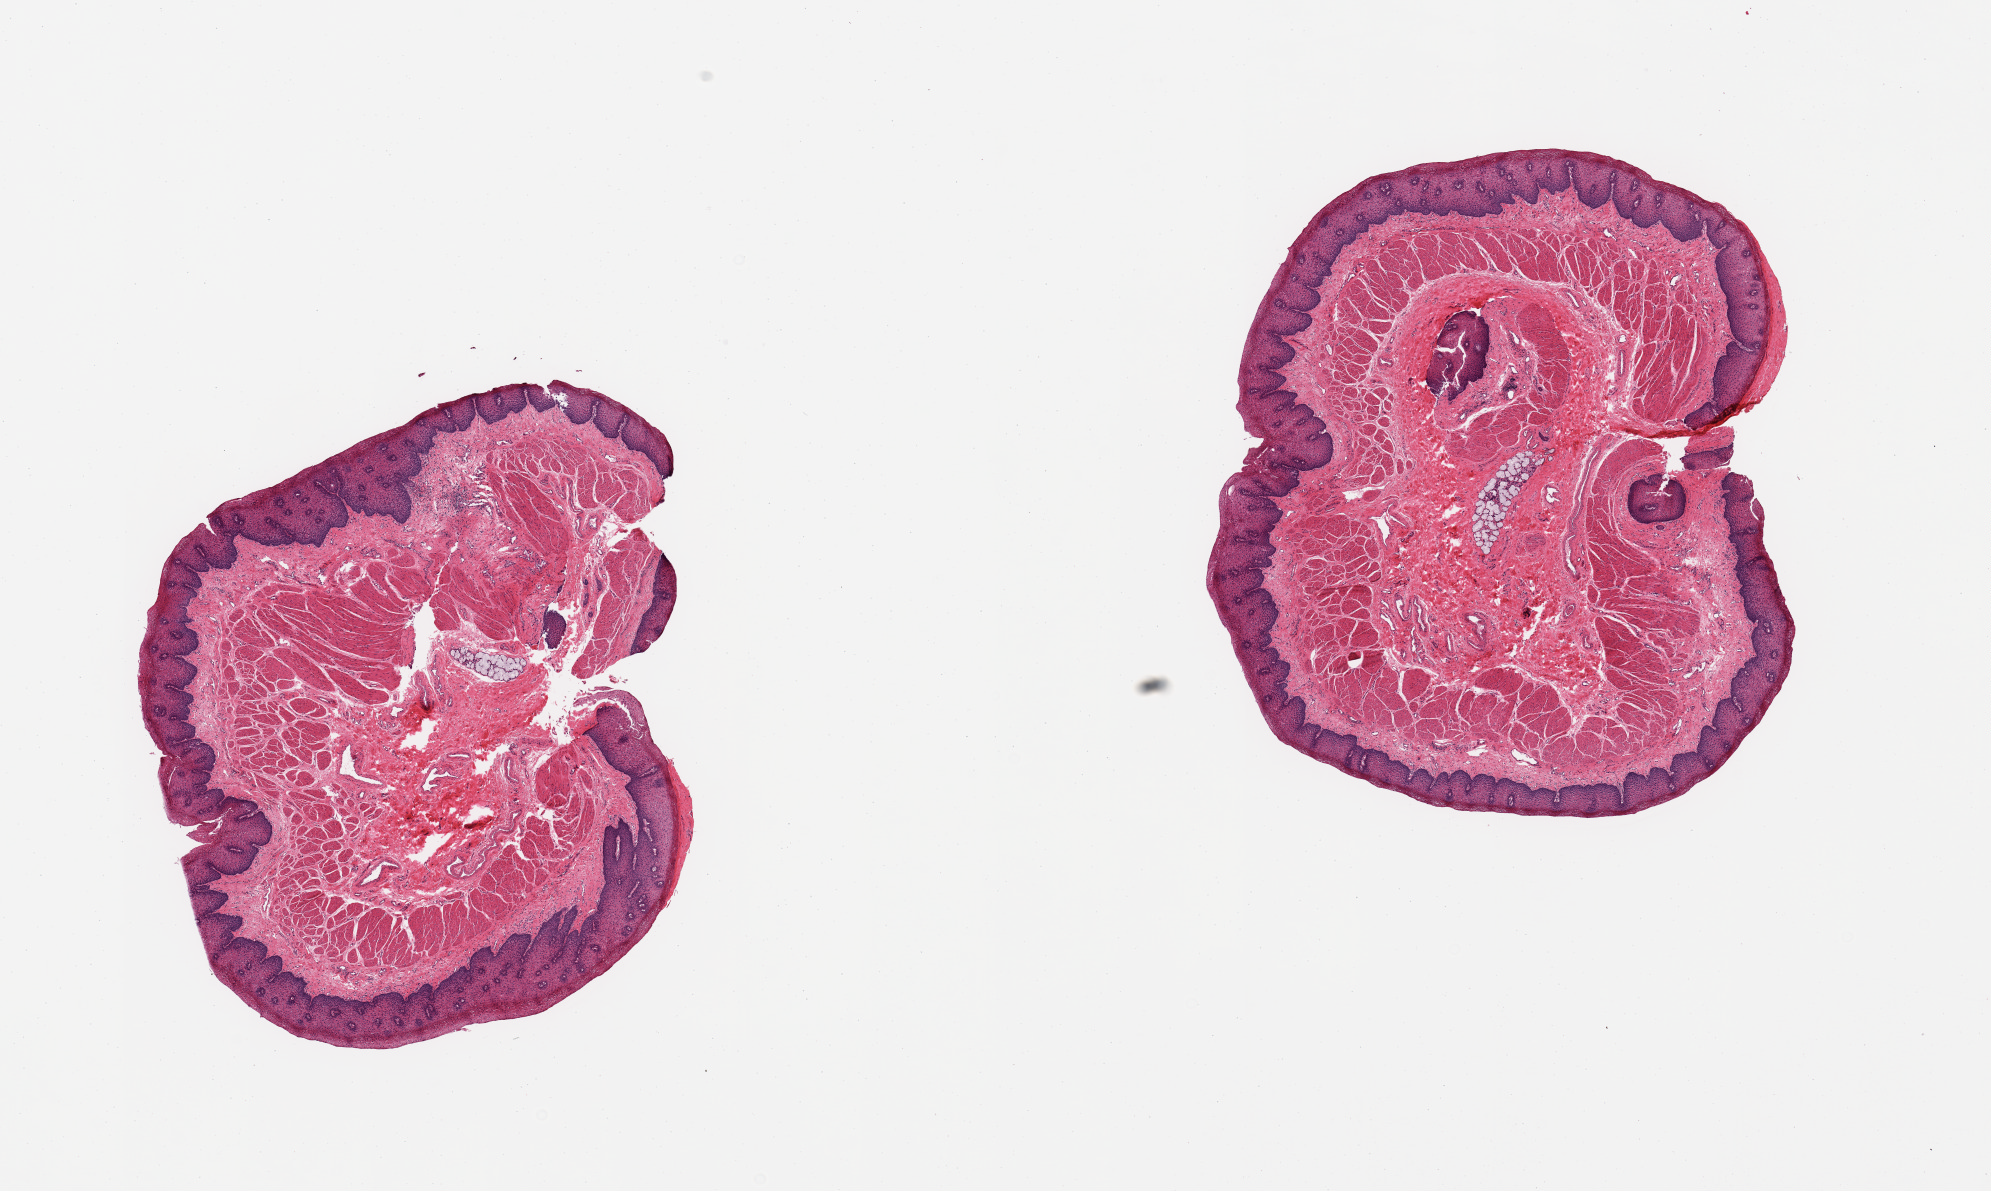
Haematoxylin and eosin whole-slide image — low-resolution overview of the scanned area, about 15.8 x 9.4 mm (acquisition: 20x scan), PAXgene-fixed paraffin-embedded (PFPE) section, section of esophageal mucous membrane (target tissue), tissue donor sample. Donor: male.
* reviewer comment on this tissue sample: 2 pieces, squamous mucosa up to ~0.3mm